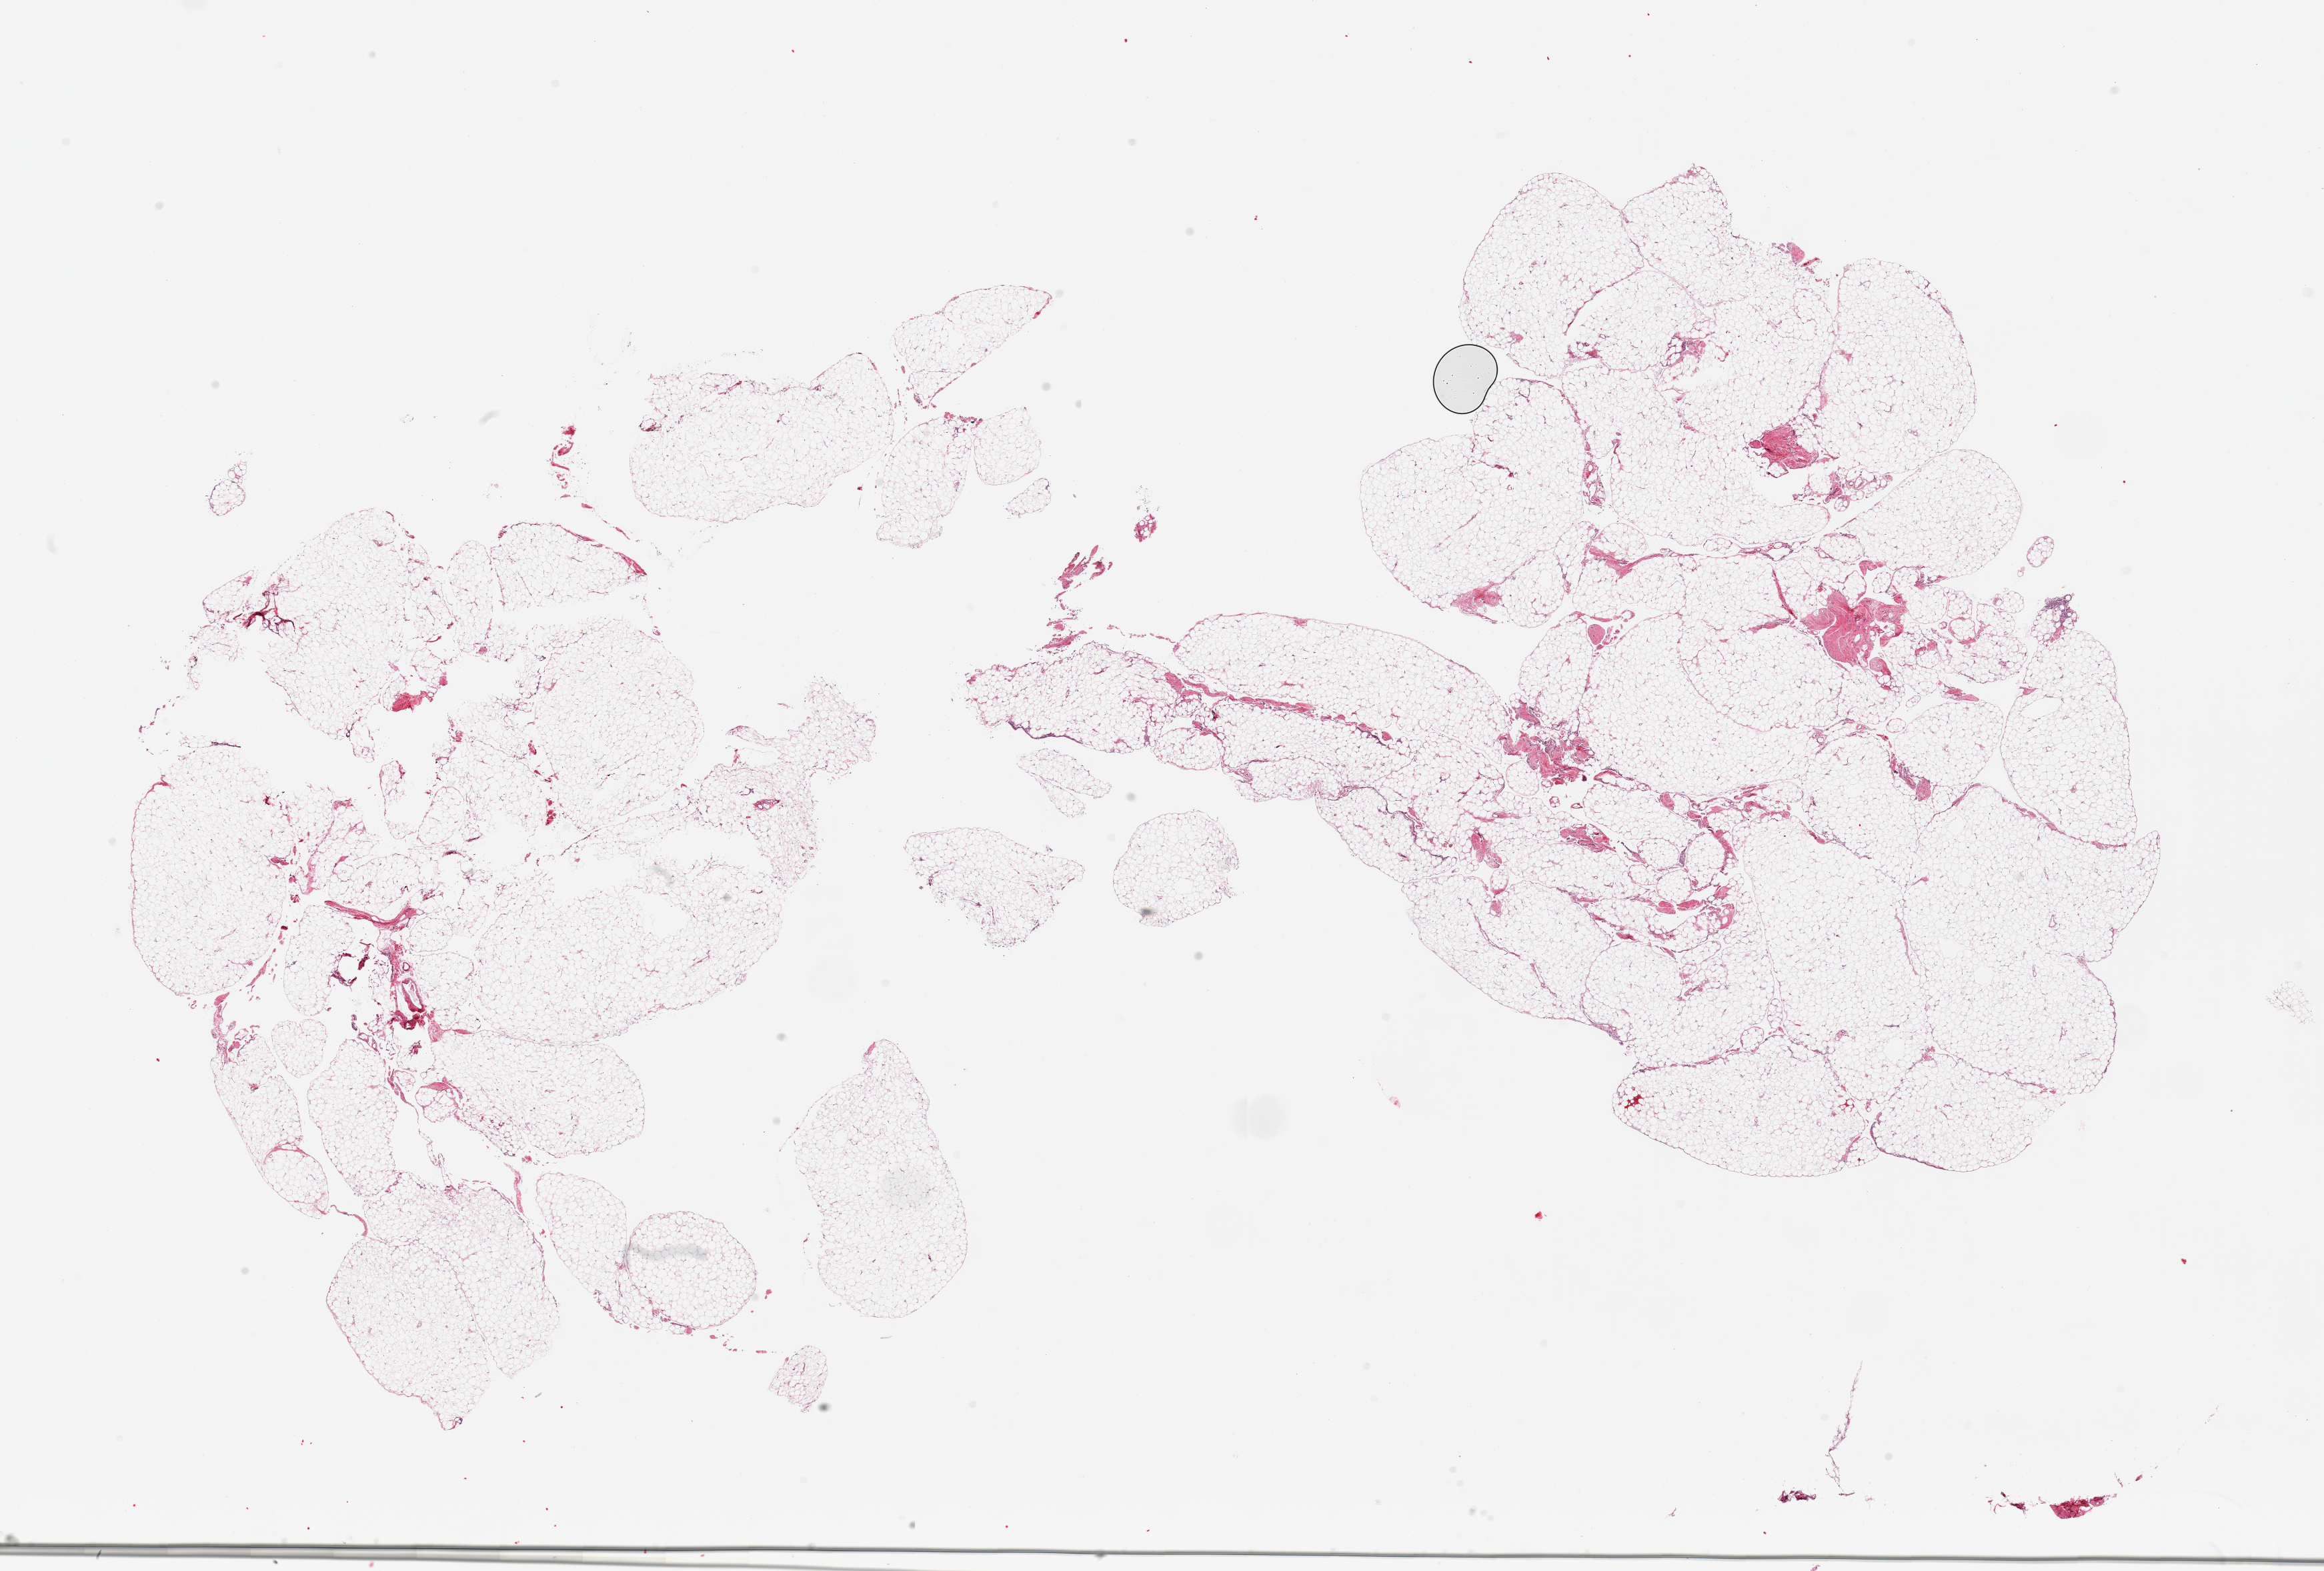
Digitized hematoxylin and eosin (H&E)-stained section — low-resolution overview of the scanned area, about 27.6 x 18.6 mm; PAXgene-fixed paraffin-embedded (PFPE) section; sampled site (target tissue): omentum; donor tissue sample. Donor: male.
• pathologist's review note for this sample: 2 pieces, ~5% fasca; Minute focus of mesothelial hyerplasia